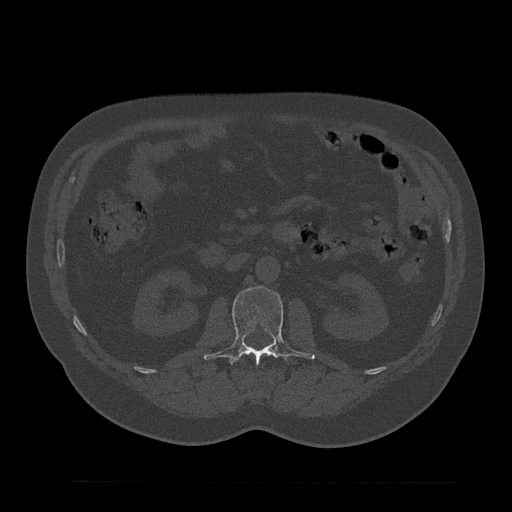
CT including the spine, one axial slice. Position 106 of 797 along the scan axis. Reconstruction kernel Br40s/3. 120 kVp. Bone window (W 1800 / L 400 HU). 512 × 512 image matrix, field of view 430 × 430 mm. Patient: male, 61 years. Case-level facts recorded for this patient, not image findings: primary cancer: prostate.
Structures marked on this image (semi-automatically segmented with operator editing):
- L1 vertebra: bounding box <263,352,273,356> (left, top, right, bottom; pixels)
- L2 vertebra: <204,286,315,366>